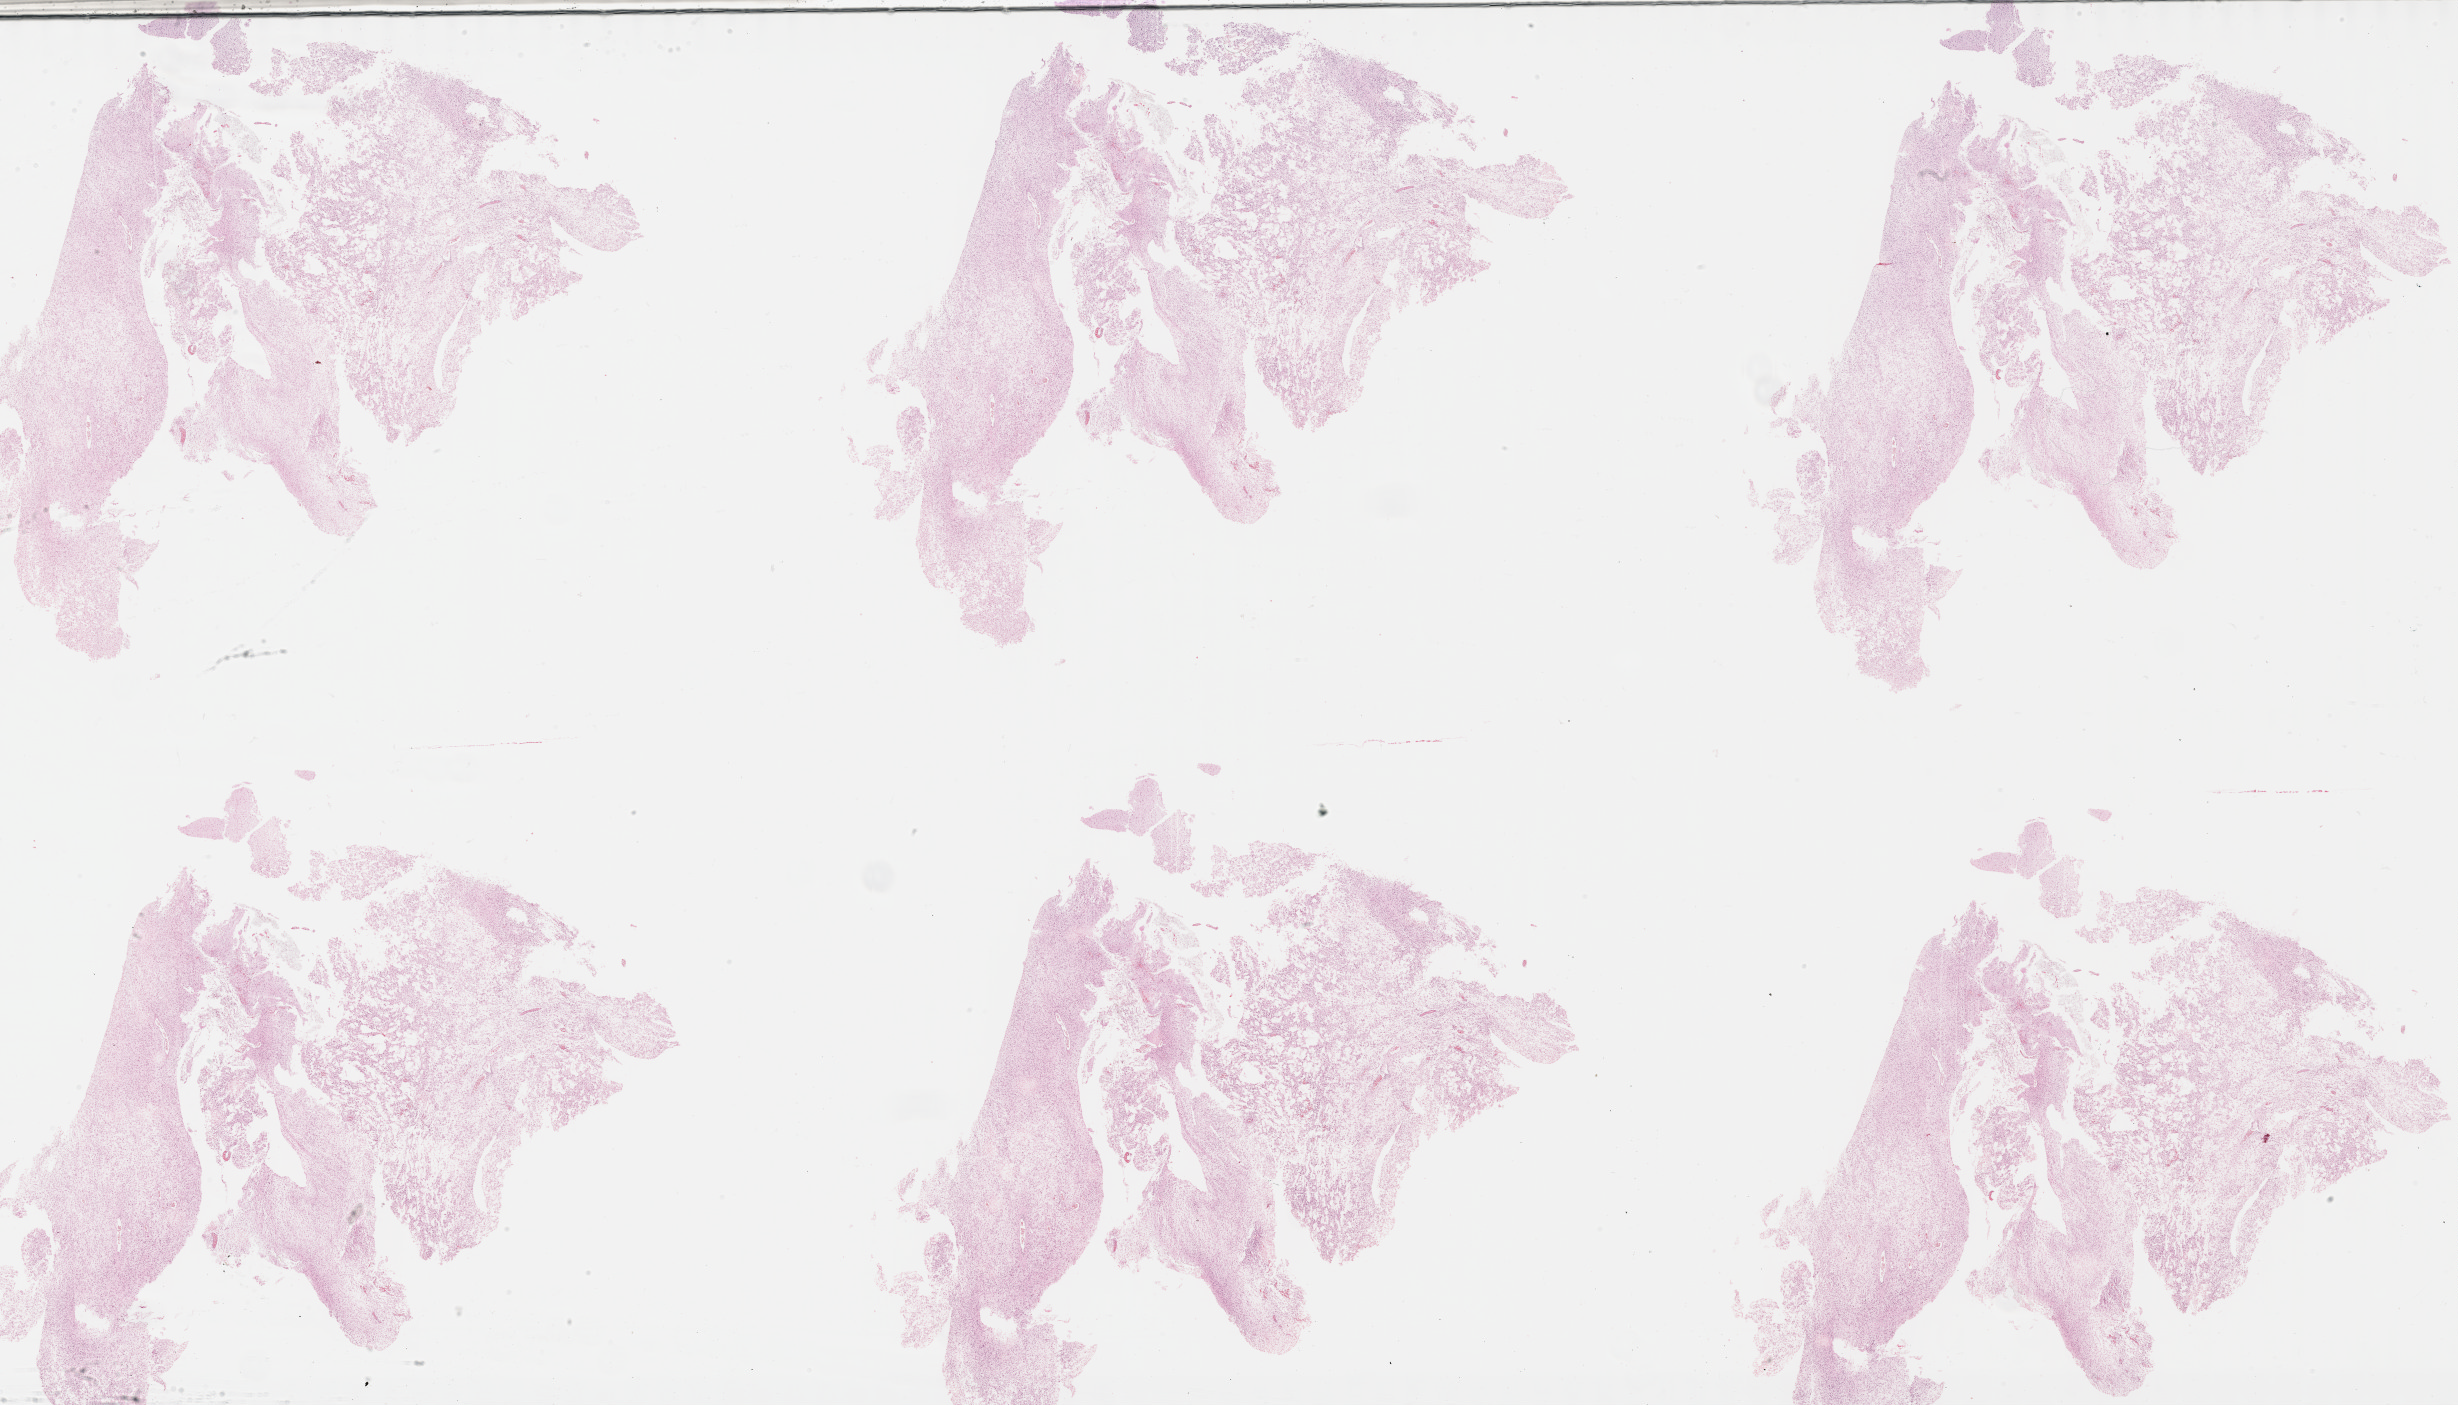
Digitized H&E-stained tissue section (whole slide) — low-resolution overview of the scanned area, about 39.7 x 22.7 mm (from a 40x scan); formalin-fixed paraffin-embedded (FFPE) diagnostic section; sample: recurrent tumour, brain. Male, age 29 years at initial diagnosis.
This section: recurrent tumour. Patient diagnosis: Oligodendroglioma, NOS (cerebrum).